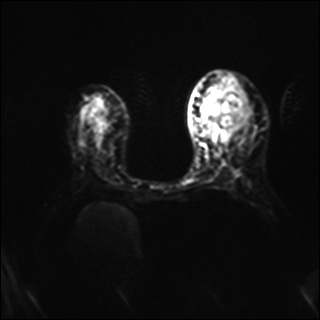
Breast MRI, one axial slice. Position 20 of 40 along the scan axis. Diffusion-weighted series; image 2 of 4 stored at this slice position (different b-values; order by instance number). 1.5 T. 4 mm slice thickness. 320 × 320 image matrix, field of view 320 × 320 mm. Female patient.
Annotated regions visible in this slice (expert manual segmentation):
- tumour on diffusion-weighted imaging: bounding box (x1, y1, x2, y2) in pixels: (219, 112, 239, 128)